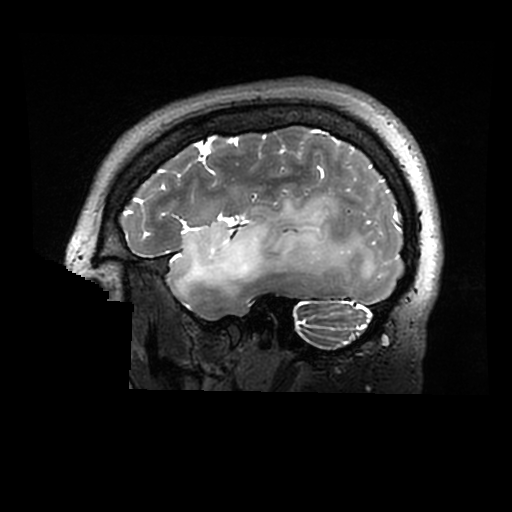
Brain MRI from a brain-tumour surgery series, one sagittal slice; position 229 of 320 along the scan axis; 0.6 mm slice thickness; 512 × 512 image matrix. Case-level facts recorded for this patient, not image findings: histopathology: Astrocytoma; WHO grade: 2; IDH mutation: yes.
Outlined on this slice (outlined manually by an expert reader):
- tumour: bounding box [x1, y1, x2, y2] px = [169, 195, 379, 295]